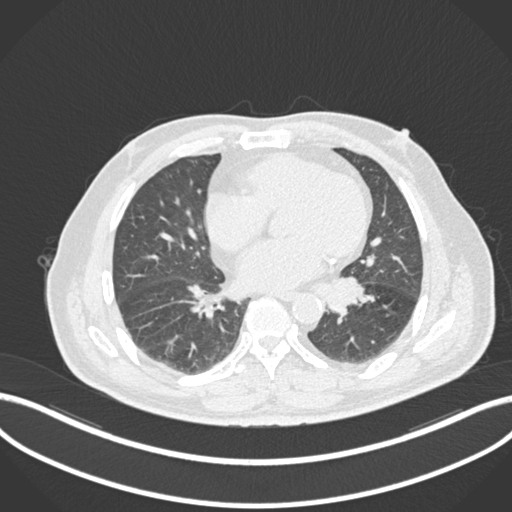
Chest CT, one axial slice; position 52 of 161 along the scan axis; reconstruction kernel B30f; lung window (W 1500 / L -600 HU); 512 × 512 image matrix. Patient: male, 71 years. Case-level facts recorded for this patient, not image findings: clinical TNM (as recorded): T1b N0 M0.
Outlined on this slice (bounding box drawn by a radiologist):
- lung tumour (recorded histology: squamous cell carcinoma): box from (x=320, y=274) to (x=368, y=322) px